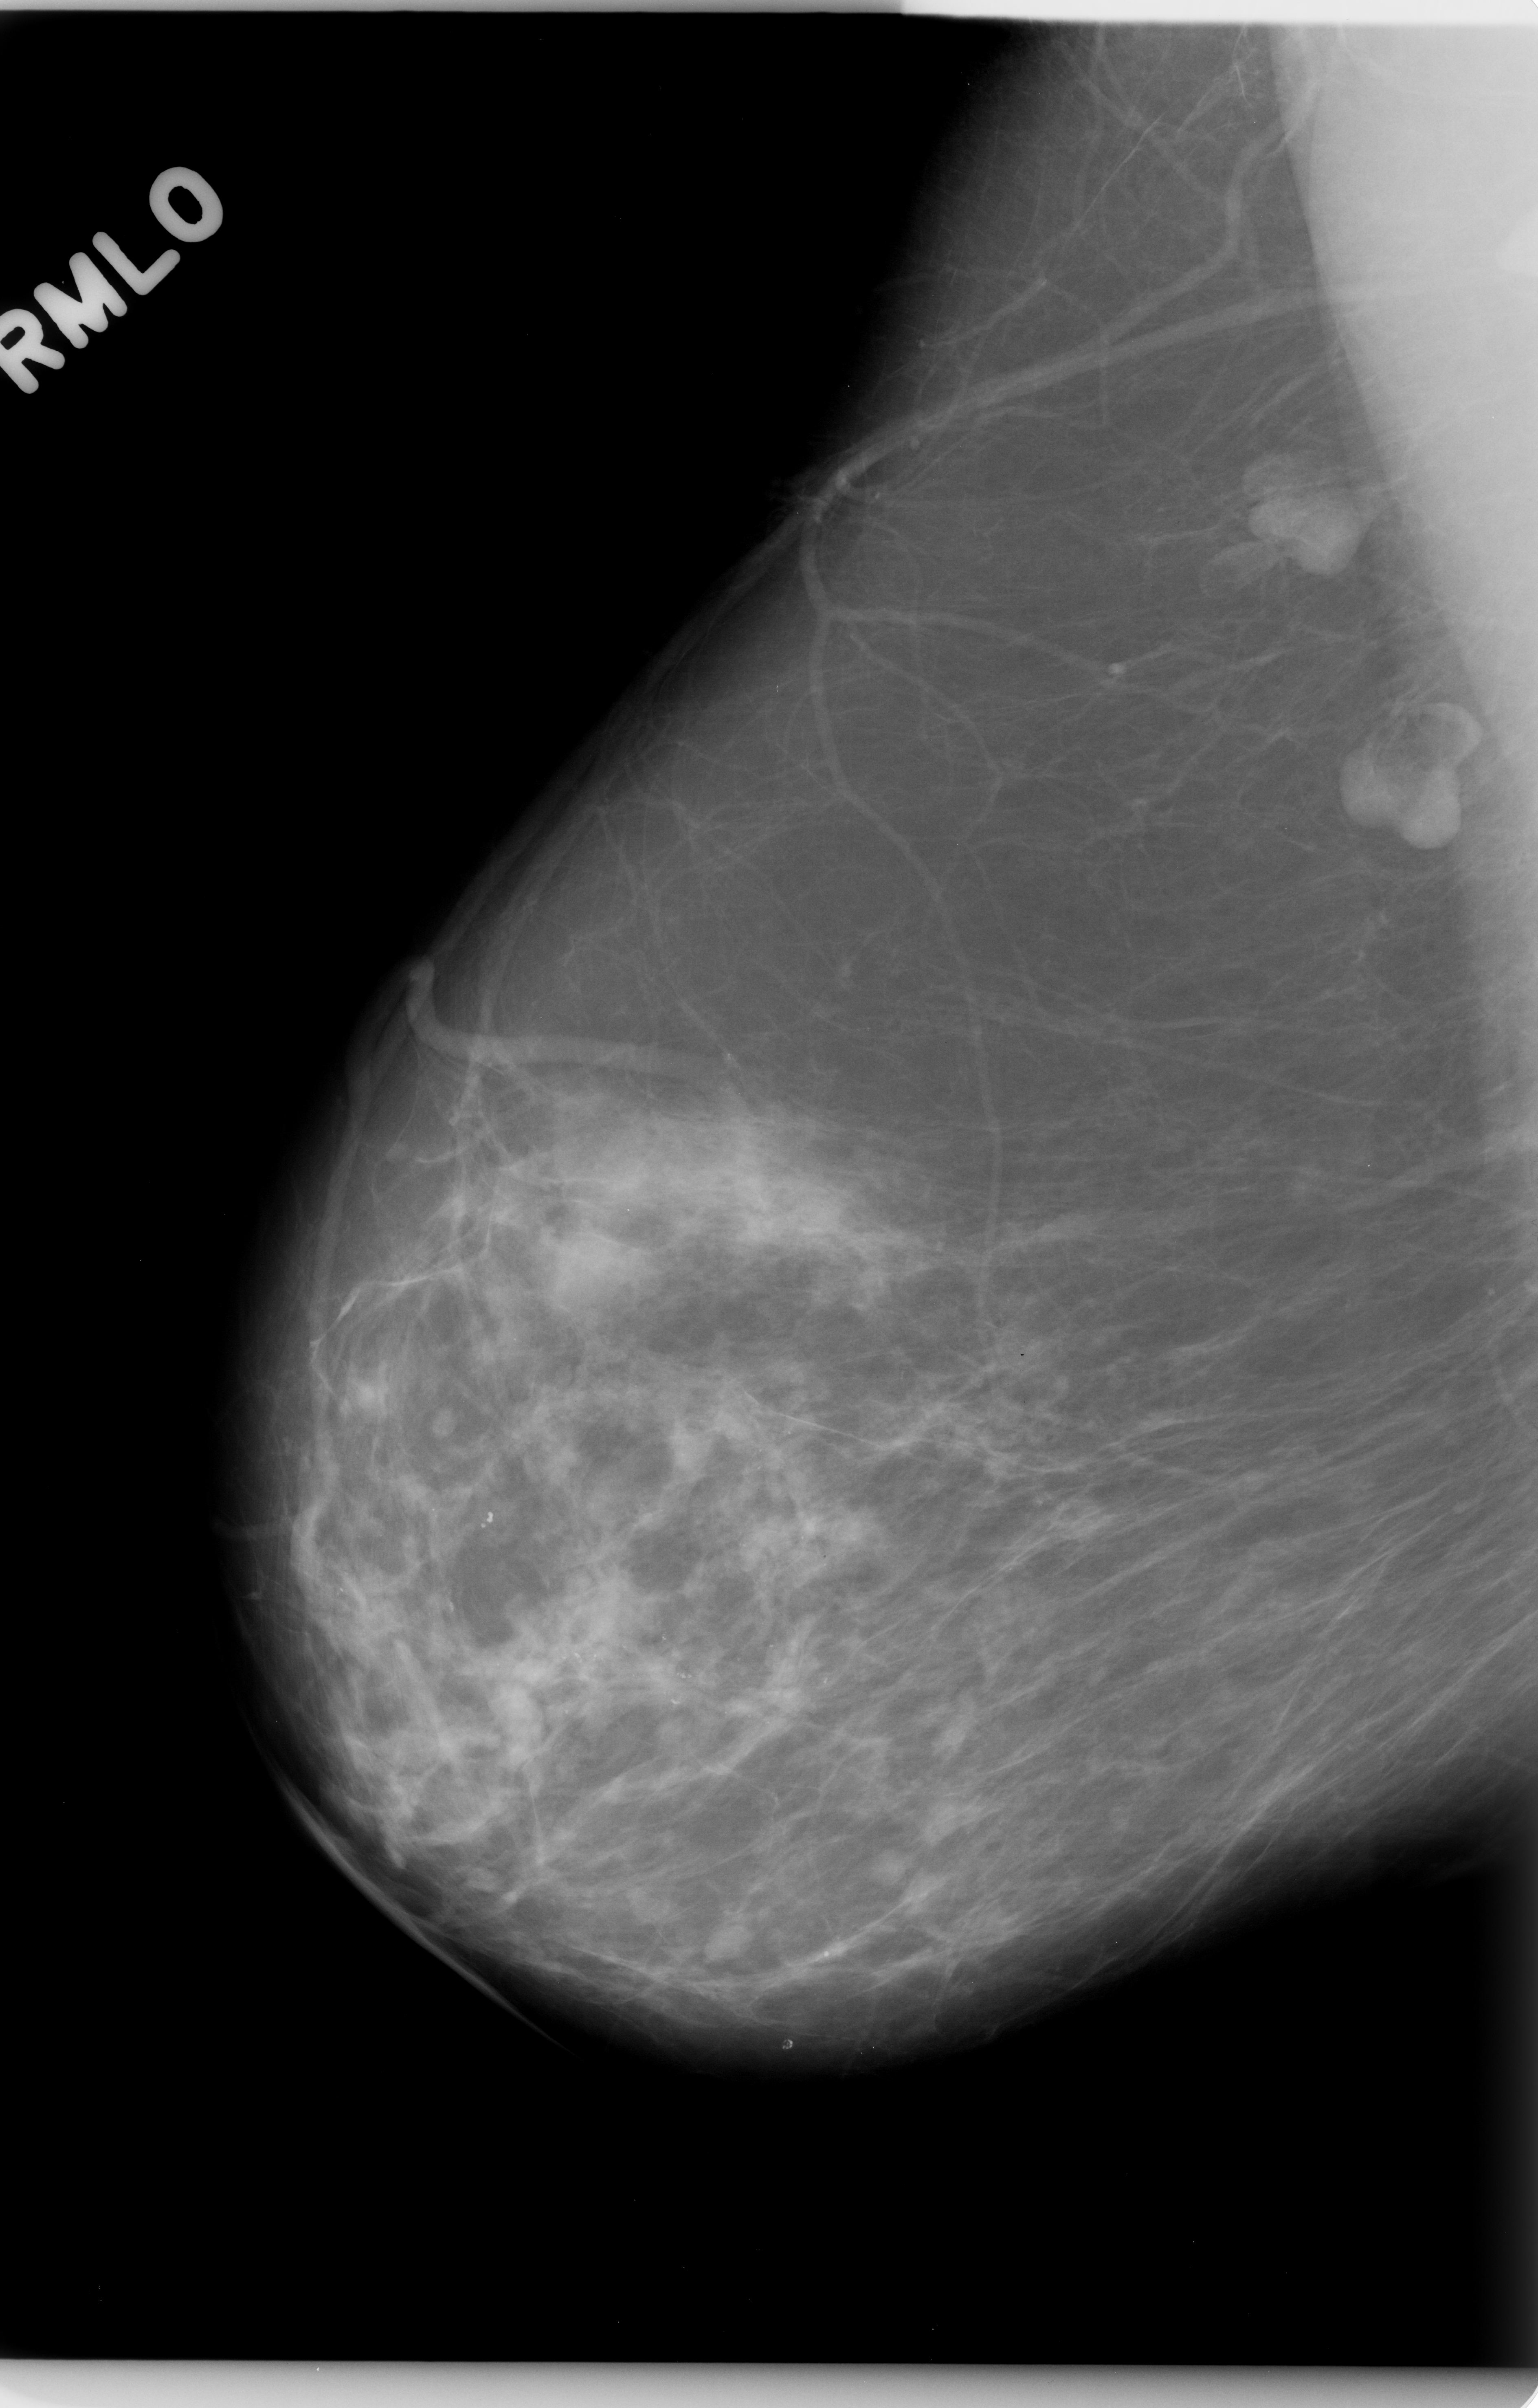
Digitized screen-film mammogram, right breast, mediolateral oblique (MLO) view.
Abnormality record for this image: calcifications, morphology pleomorphic, distribution segmental; BI-RADS assessment category 4; subtlety rating 4 on a 1 (subtle) to 5 (obvious) scale; pathology (as recorded): malignant.